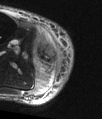
MRI of an extremity soft-tissue mass, one axial slice. Position 15 of 48 along the scan axis. T2-weighted fat-saturated. MR volume resampled by the dataset authors to the PET/CT grid (not the native acquisition matrix). 3.27 mm slice thickness. 102 × 119 image matrix. Male patient. Case-level facts recorded for this patient, not image findings: histological type: pleiomorphic liposarcoma; grade: high; site of the primary tumour: right calf.
Outlined on this slice (expert contour drawn on MRI and transferred to this co-registered scan by the dataset authors):
- gross tumour volume including surrounding oedema: box from (x=33, y=35) to (x=63, y=90) px
- gross tumour volume (mass): (x=39, y=44)–(x=56, y=63)